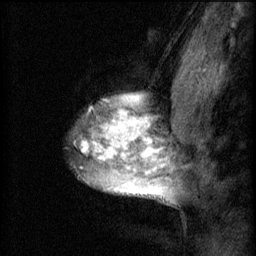
Breast MRI (dynamic contrast-enhanced), one sagittal slice; position 48 of 60 along the scan axis; 3 images stored at this slice position (order not interpretable as contrast timing); 1.5 T; TE 4.2 ms, TR 8.2 ms; 256 × 256 image matrix, field of view 180 × 180 mm. Female patient, age 40 years.
Structures marked on this image (semi-automatically segmented with operator editing):
- analysis volume of interest (the breast-tissue region the enhancement analysis was run in; not a lesion): box from (x=72, y=82) to (x=167, y=205) px
- tumour enhancement mask (voxels above the 70 % enhancement threshold inside the analysis volume of interest): (x=81, y=94)–(x=167, y=201)